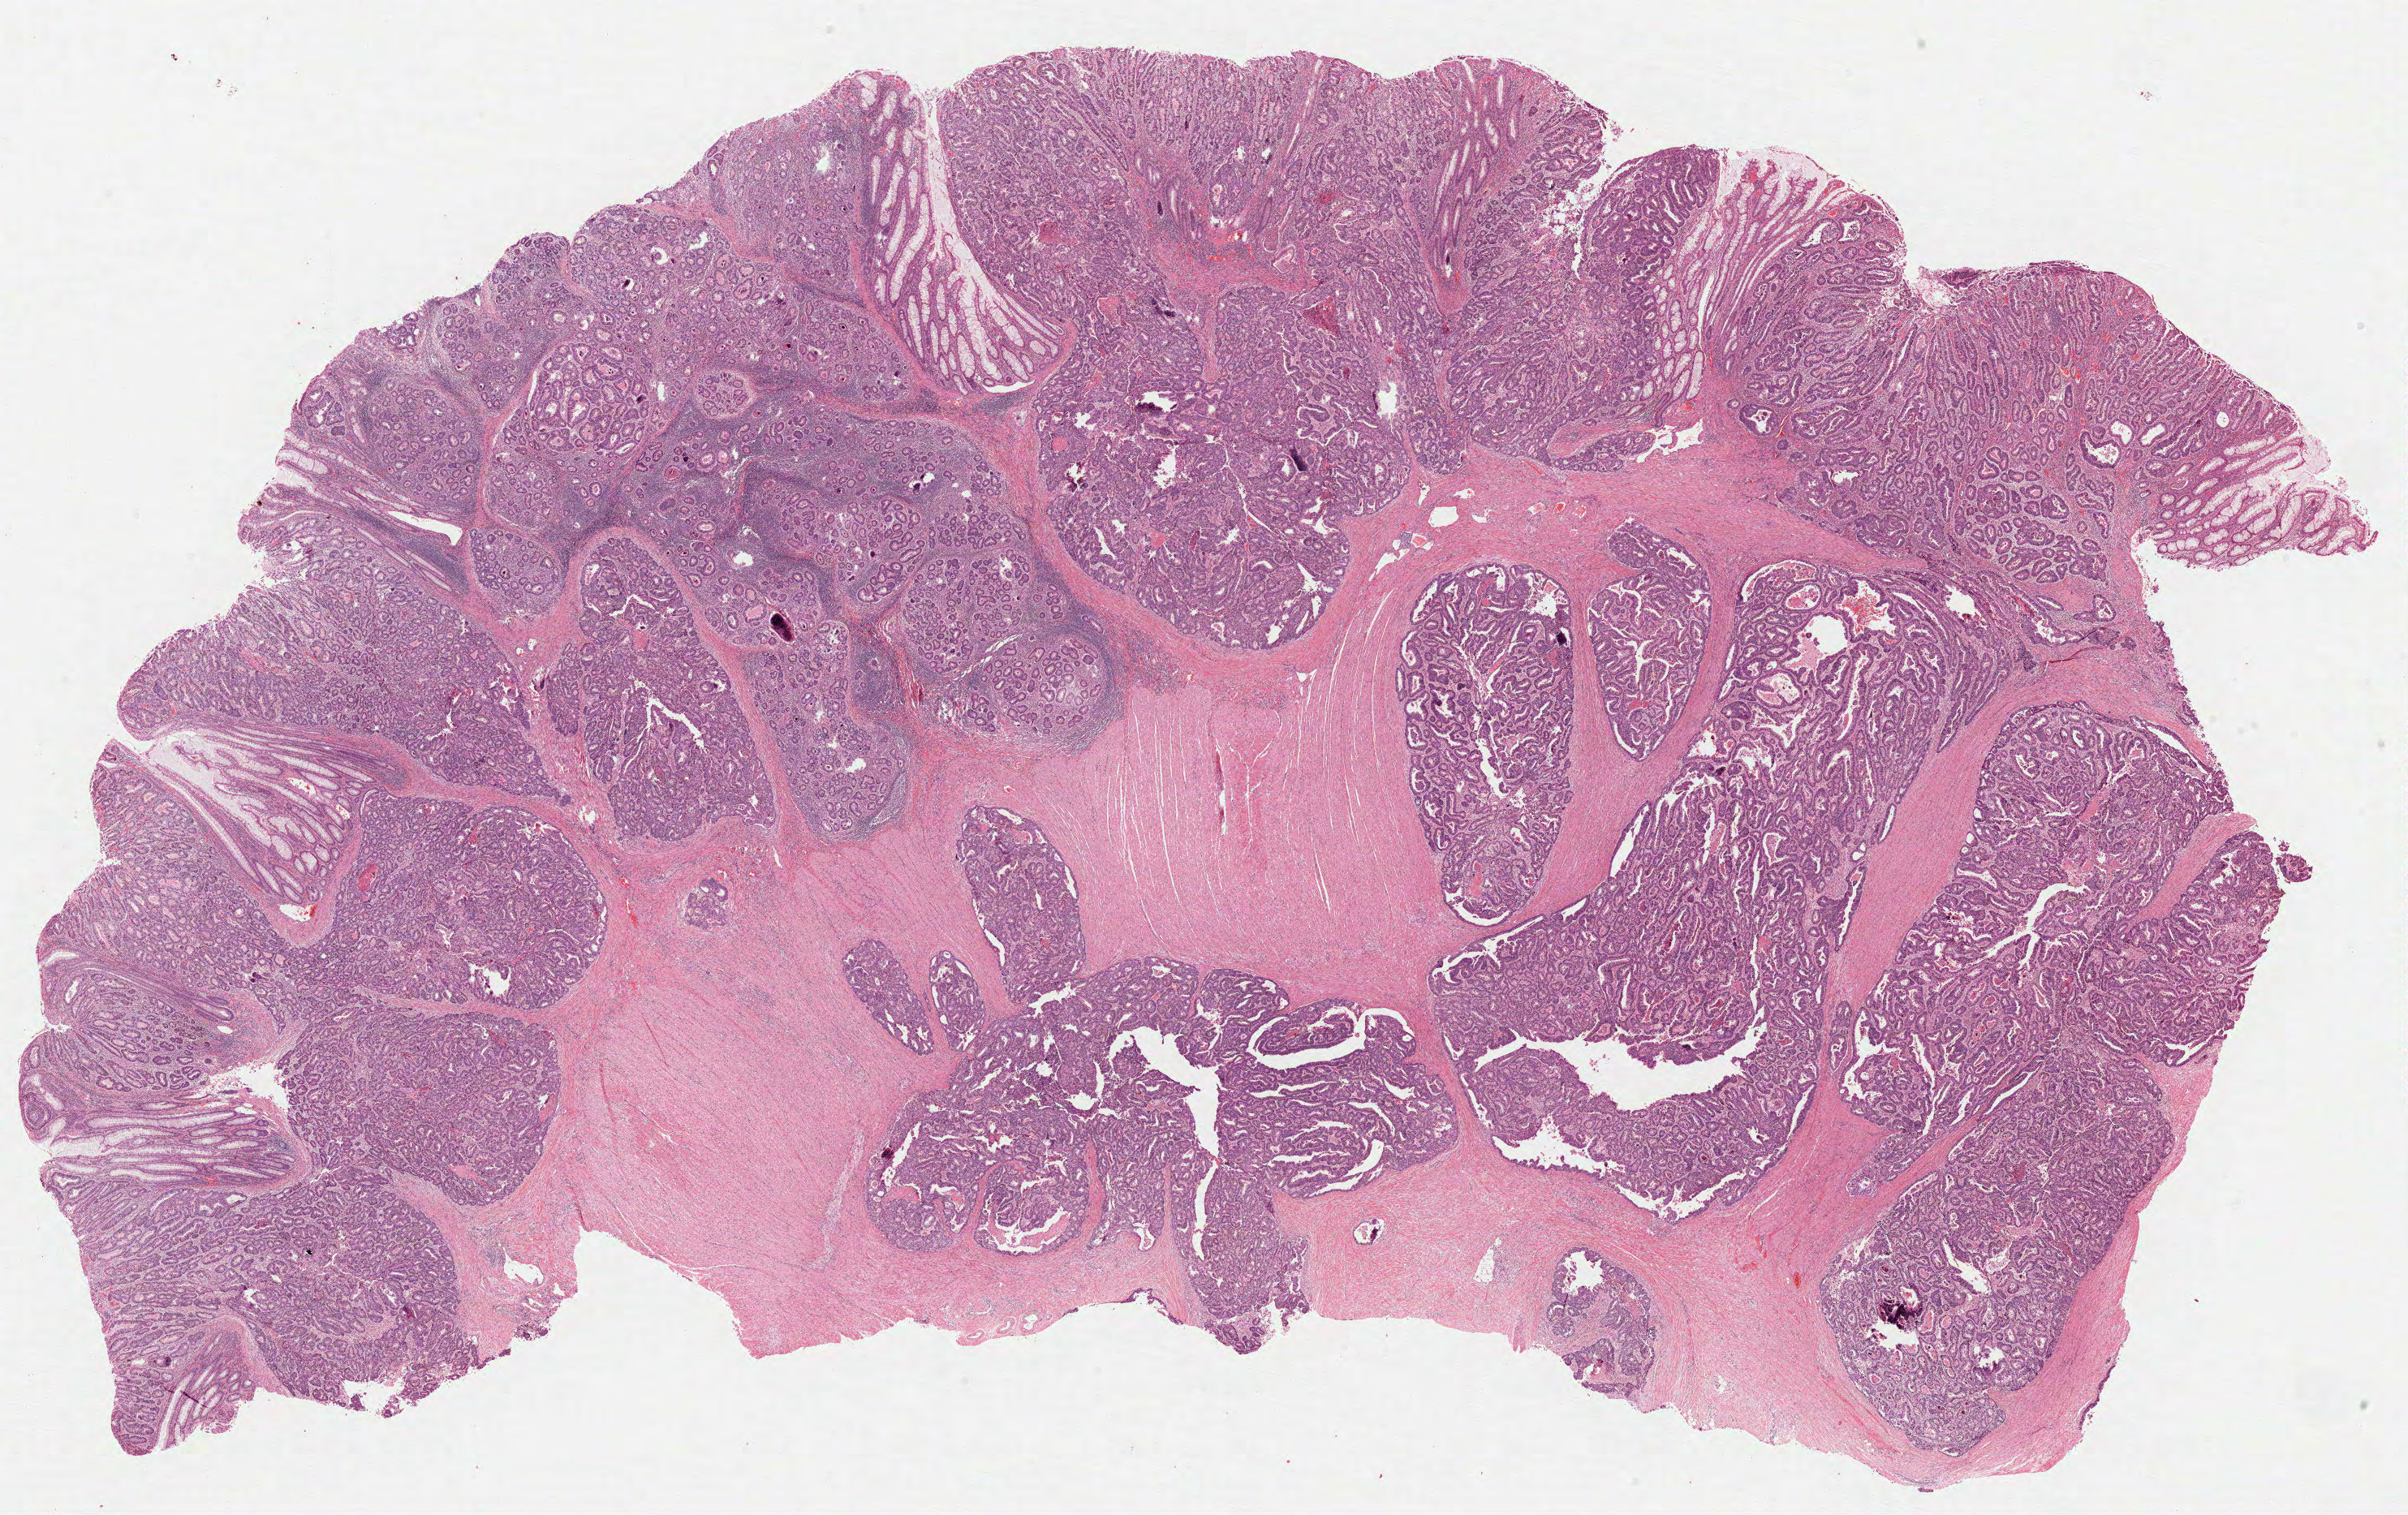
Hematoxylin and eosin (H&E) stained whole-slide image, low-resolution overview of the scanned area, about 23.9 x 15.1 mm. Formalin-fixed paraffin-embedded (FFPE) diagnostic section. Sample: primary tumour, colon. Female patient; age at initial diagnosis 51 years.
TNM: T3 N1 M0. Histologic diagnosis: Adenocarcinoma, NOS (sigmoid colon). Lymph nodes positive (case pathology): 1 of 6 examined. AJCC pathologic stage: IIIB.